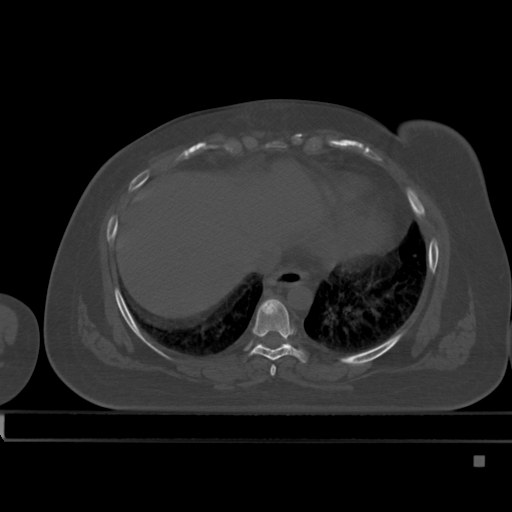
CT including the spine, one axial slice; slice 276 of 495 in the series (ordered by position); bone window (W 1800 / L 400 HU); 1.5 mm slice thickness; 512 × 512 image matrix, field of view 404 × 404 mm. Female patient, age 33 years. From the clinical record (not read from this slice): primary cancer: breast; vertebrae with lytic lesions (as recorded): T1.
Outlined on this slice (semi-automatically segmented with operator editing):
- T7 vertebra: bounding box (x1, y1, x2, y2) in pixels: (270, 365, 276, 376)
- T8 vertebra: (244, 297, 306, 363)